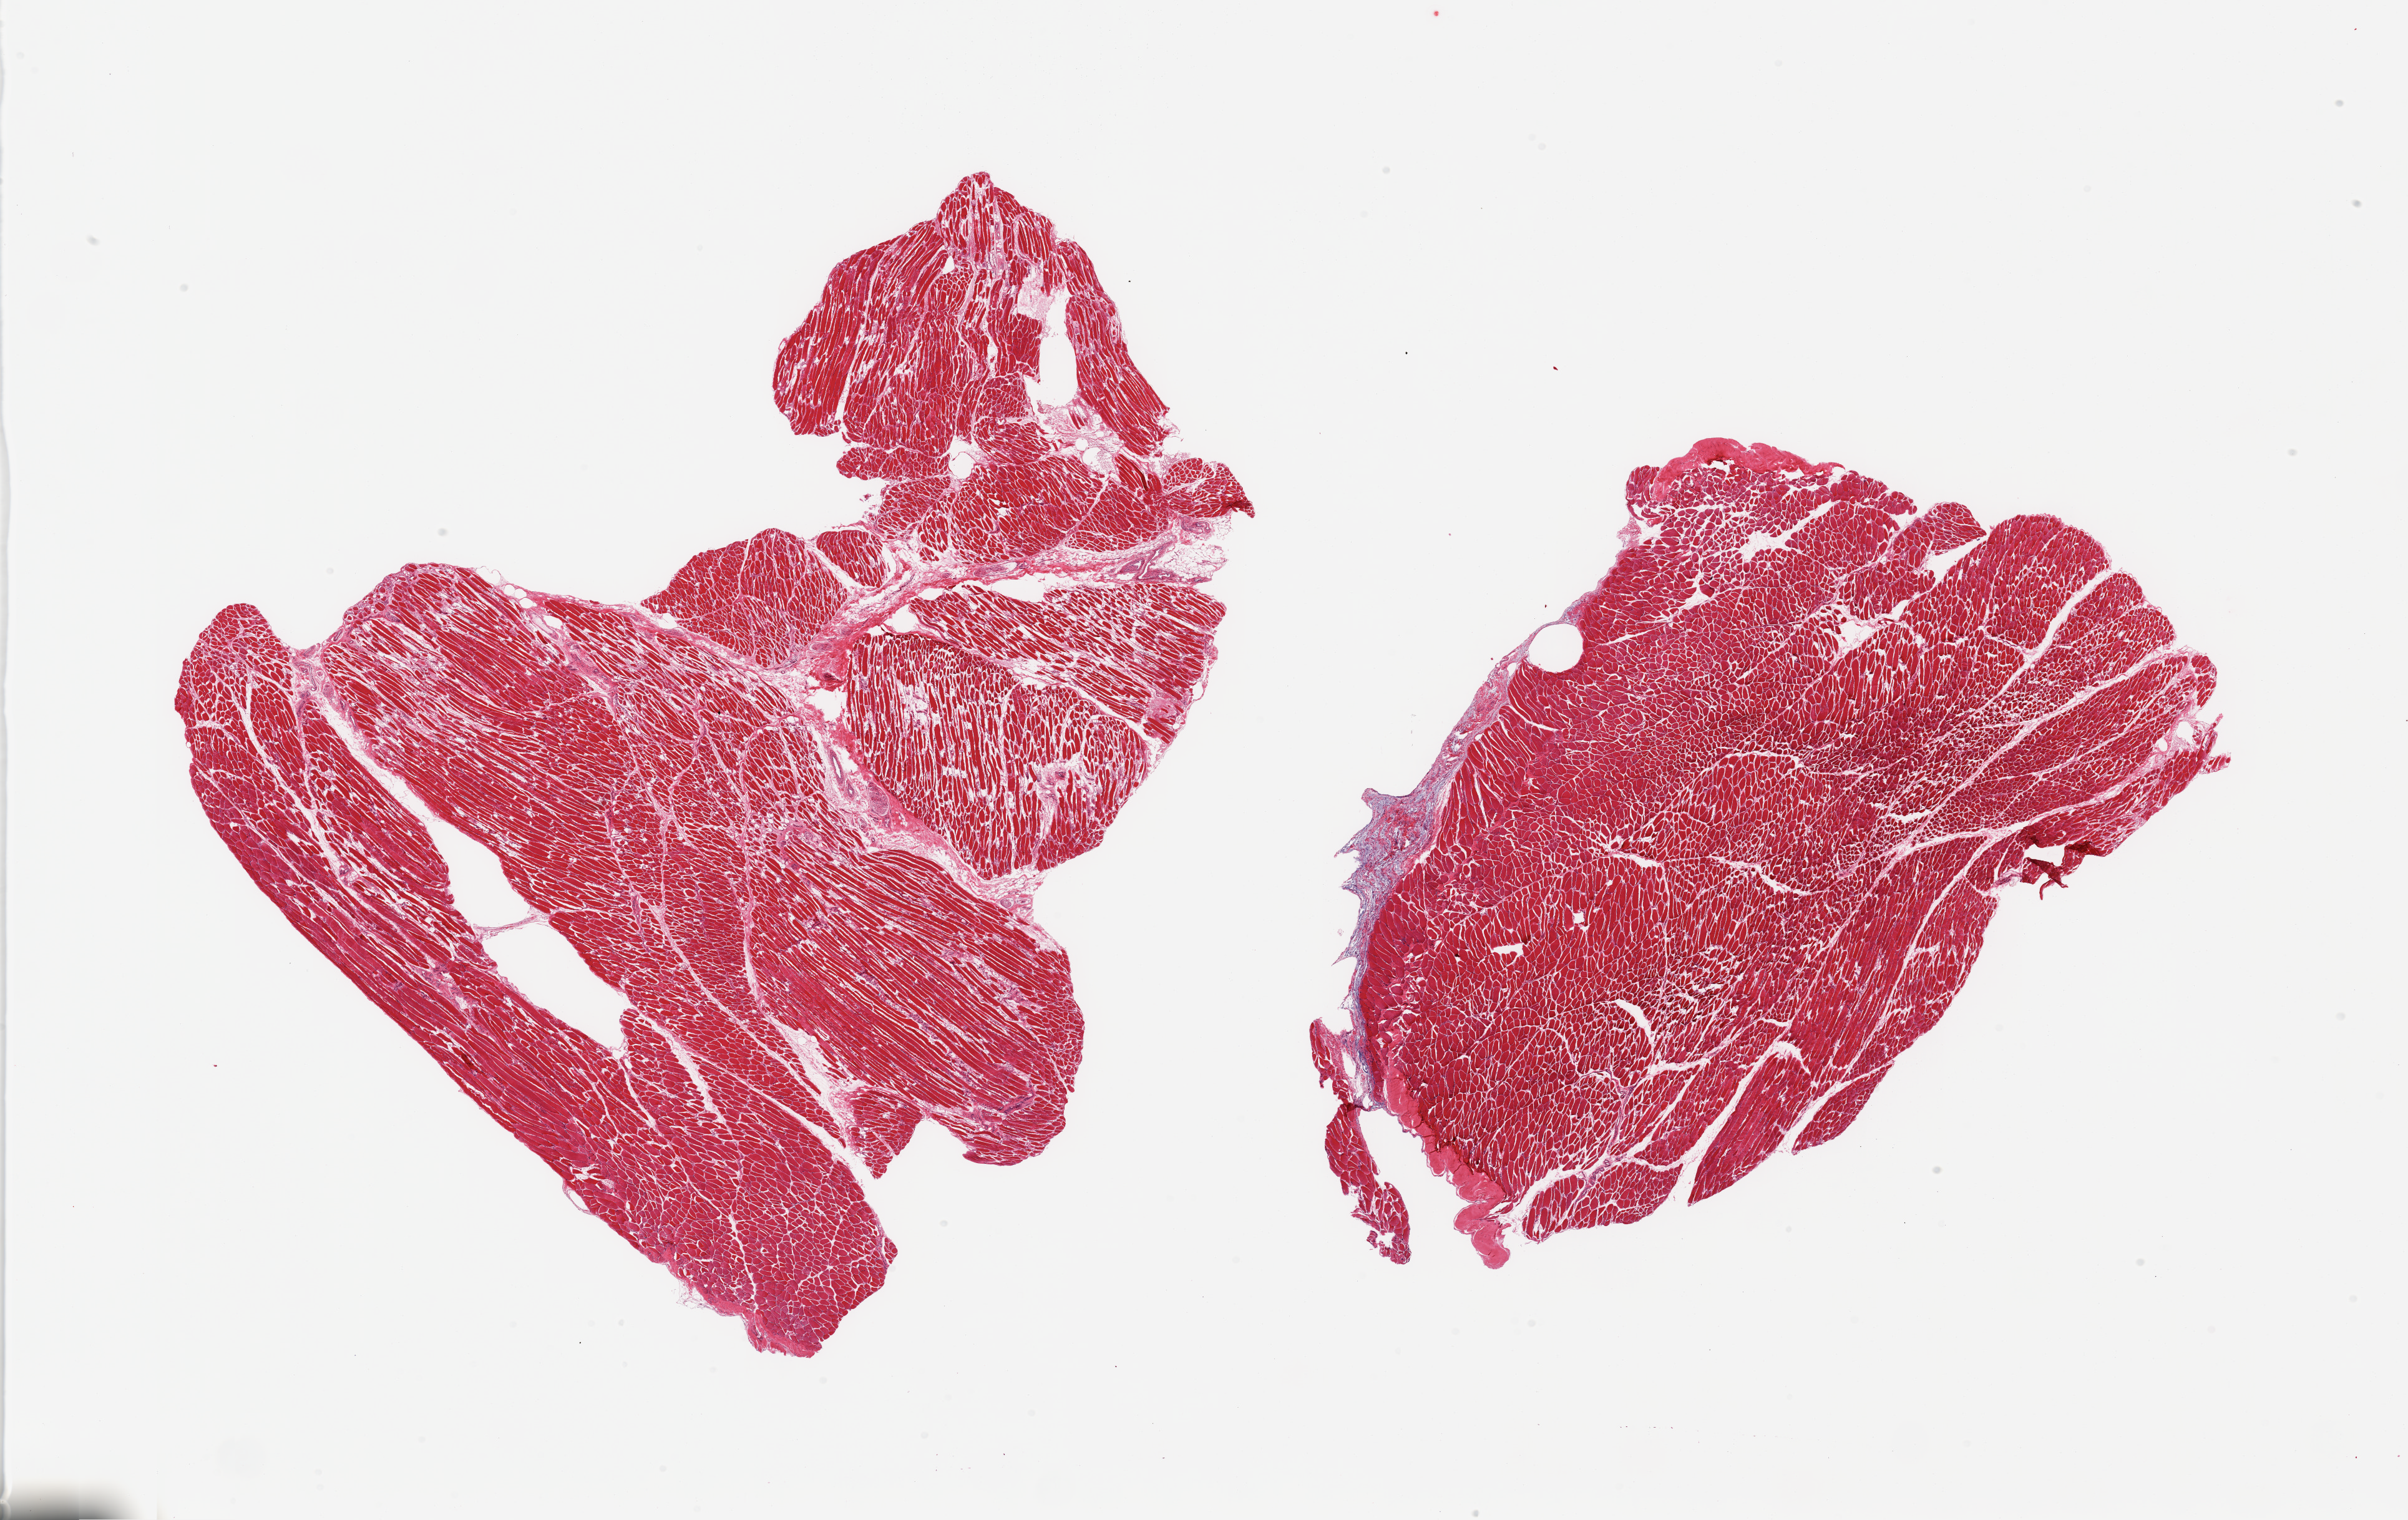
Whole-slide image, haematoxylin and eosin stain, shown as a low-resolution overview of the whole scanned area (about 30.5 x 19.3 mm); PAXgene-fixed paraffin-embedded (PFPE) section; target tissue: skeletal muscle; tissue donor sample. Male donor.
* review note (as recorded): 2 pieces